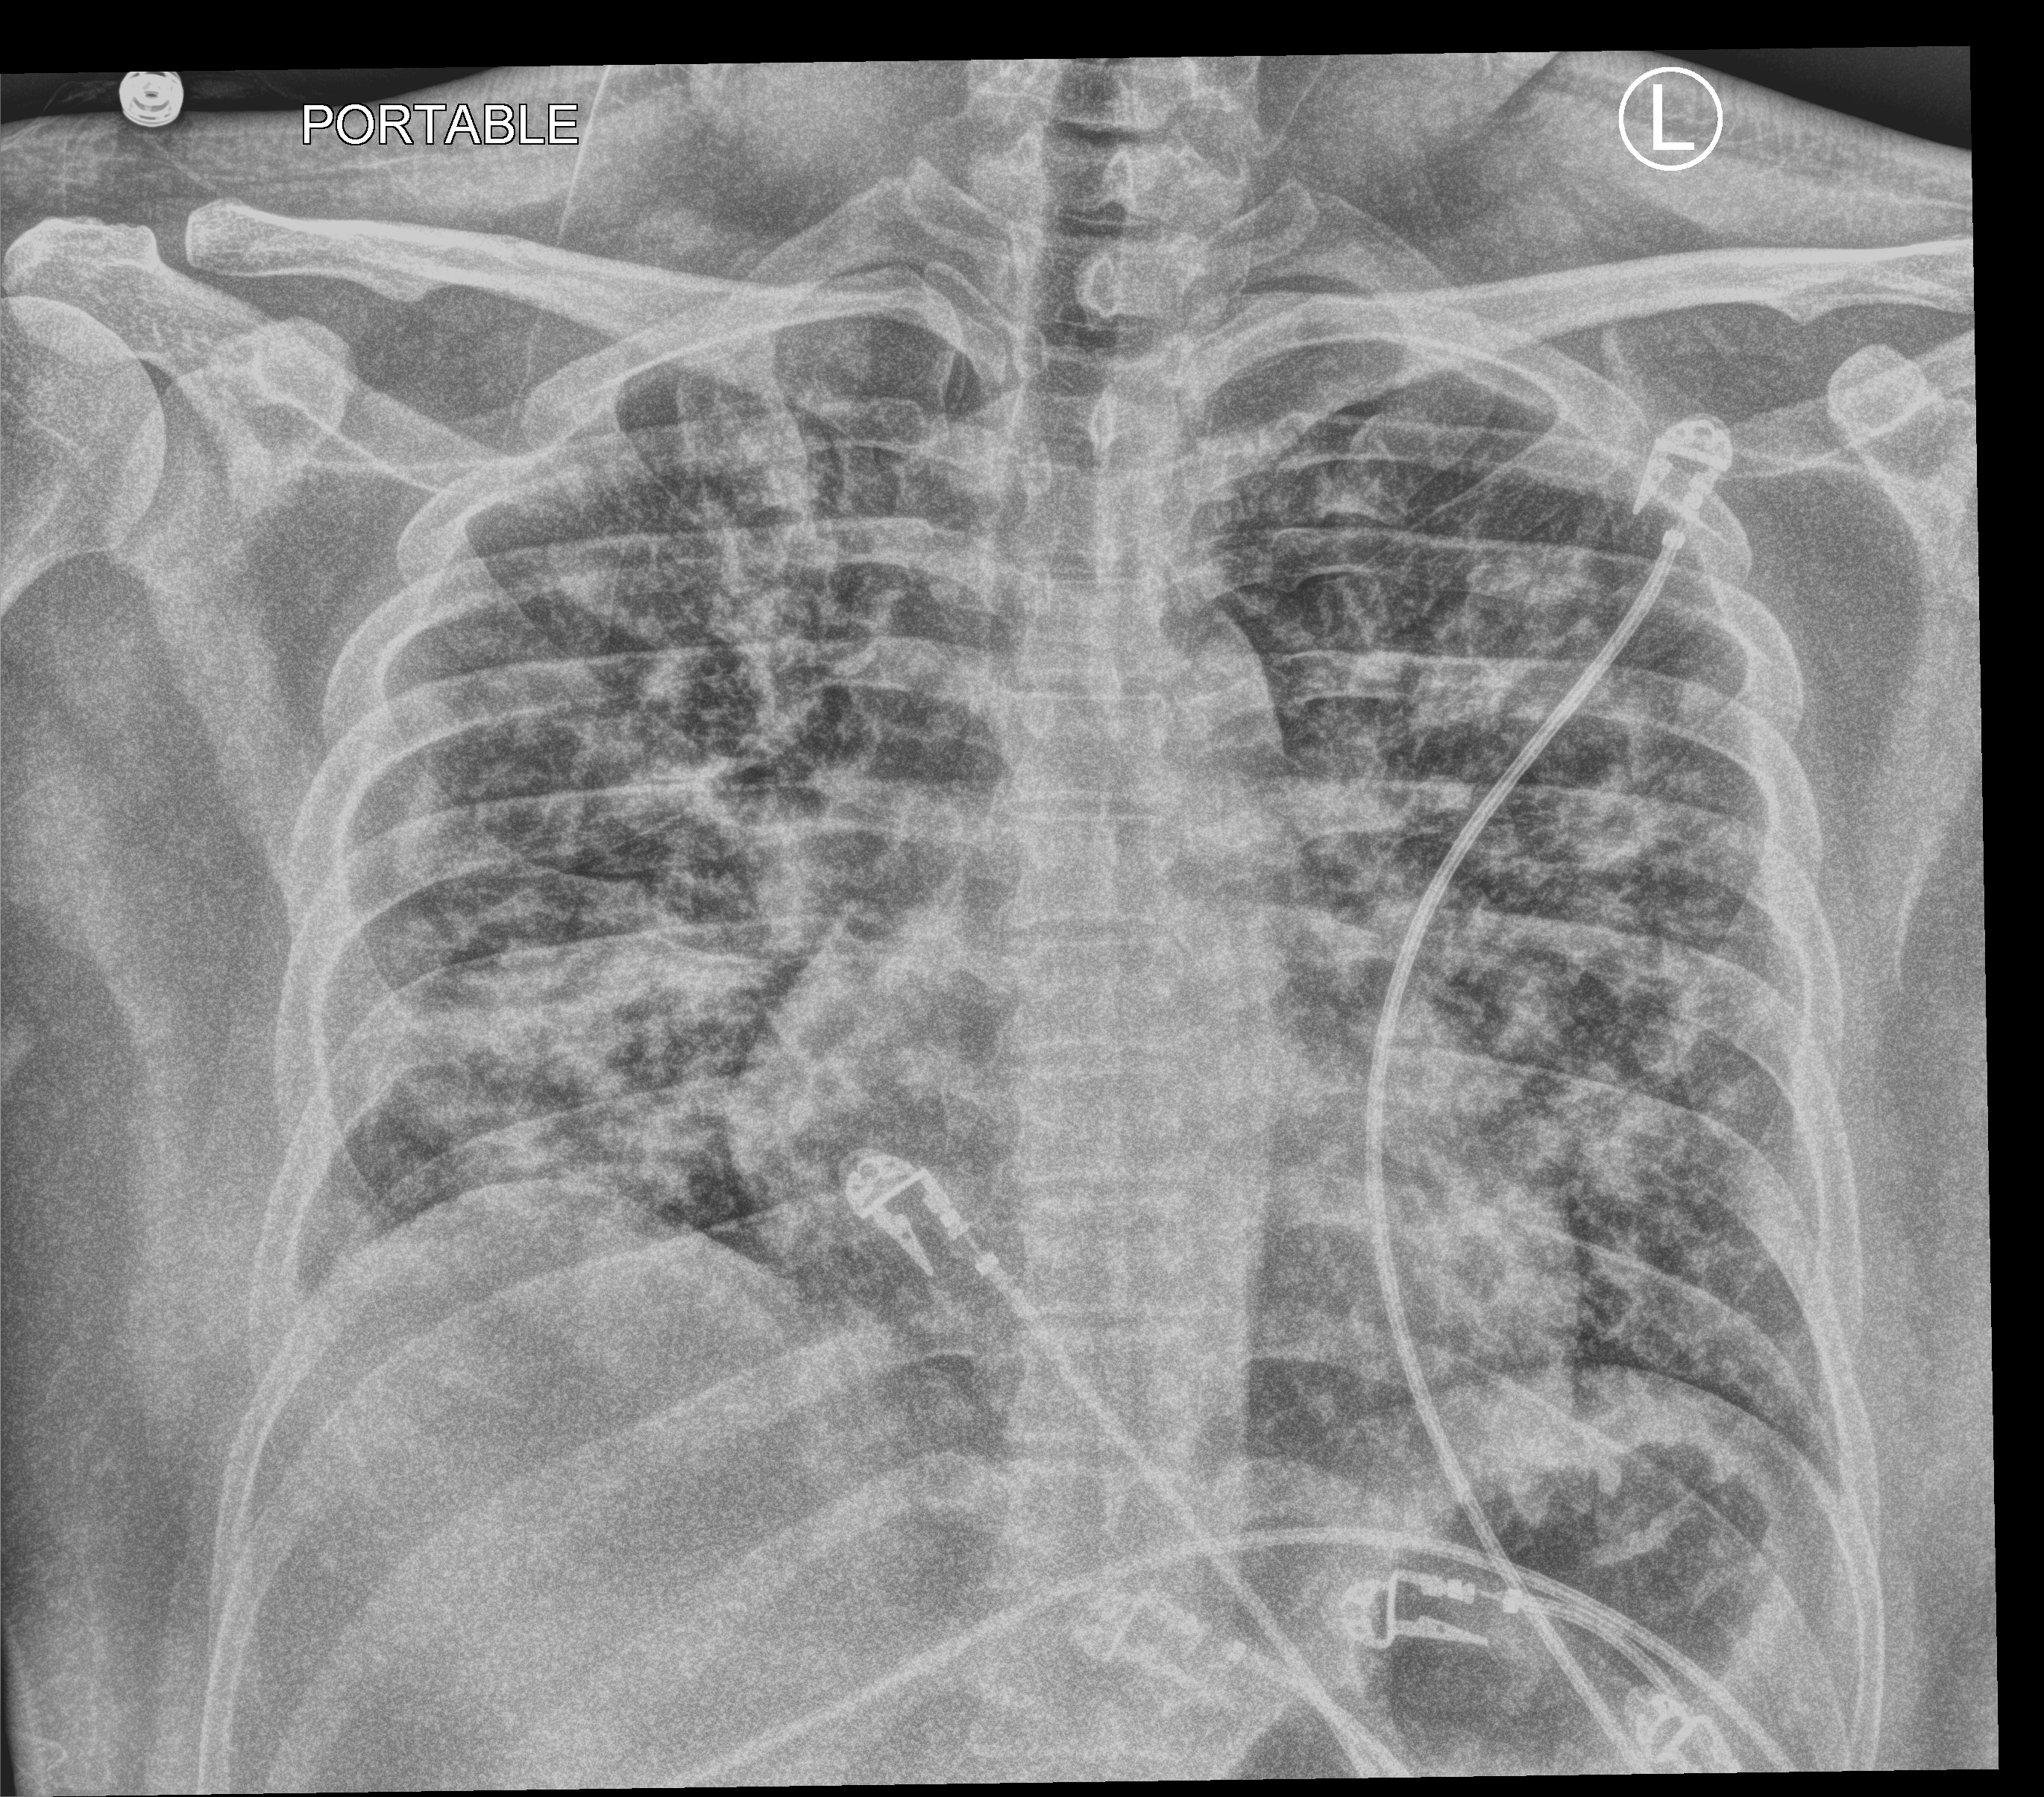
Portable chest radiograph, anteroposterior (AP) projection. Patient hospitalised with COVID-19; male, aged 18–59 years.
Hospital-stay facts (about this admission, not read from this image; timing relative to this image not recorded): length of hospital stay: 17 days; hypertension (admission record): no.